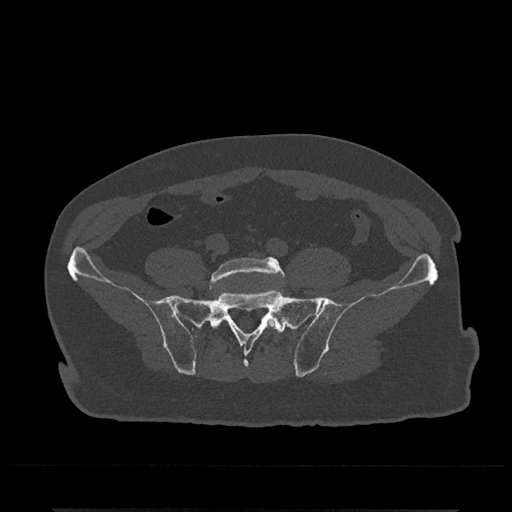
CT including the spine, one axial slice. Slice 44 of 797 in the series (ordered by position). 120 kVp. Bone window (W 1800 / L 400 HU). 512 × 512 image matrix. Patient: male, 67 years. Case-level facts recorded for this patient, not image findings: primary cancer: prostate.
Outlined on this slice (semi-automatic segmentation, software-assisted and operator-edited):
- L5 vertebra: box from (x=209, y=257) to (x=285, y=328) px